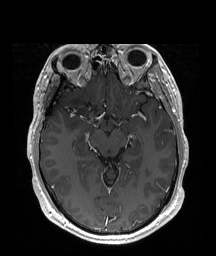
Brain MRI from a brain-tumour surgery series, one axial slice; position 115 of 192 along the scan axis; T1-weighted post-contrast; 216 × 256 image matrix, field of view 219 × 260 mm. Case-level facts recorded for this patient, not image findings: histopathology: Astrocytoma; WHO grade: 2; IDH mutation: yes.
Annotated regions visible in this slice (manually delineated by an expert):
- tumour: bounding box [x1, y1, x2, y2] px = [67, 98, 91, 132]